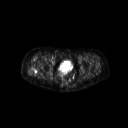
FDG PET of an extremity soft-tissue mass (from a PET/CT study), one axial slice. 3.27 mm slice thickness. 128 × 128 image matrix, field of view 600 × 600 mm. Patient: female, 57 years. From the clinical record (not read from this slice): histological type: epithelioid sarcoma with vascular differentiation; site of the primary tumour: right buttock.
Structures marked on this image (expert contour drawn on MRI and transferred to this co-registered scan by the dataset authors):
- gross tumour volume (mass): bounding box [x1, y1, x2, y2] px = [26, 65, 42, 79]